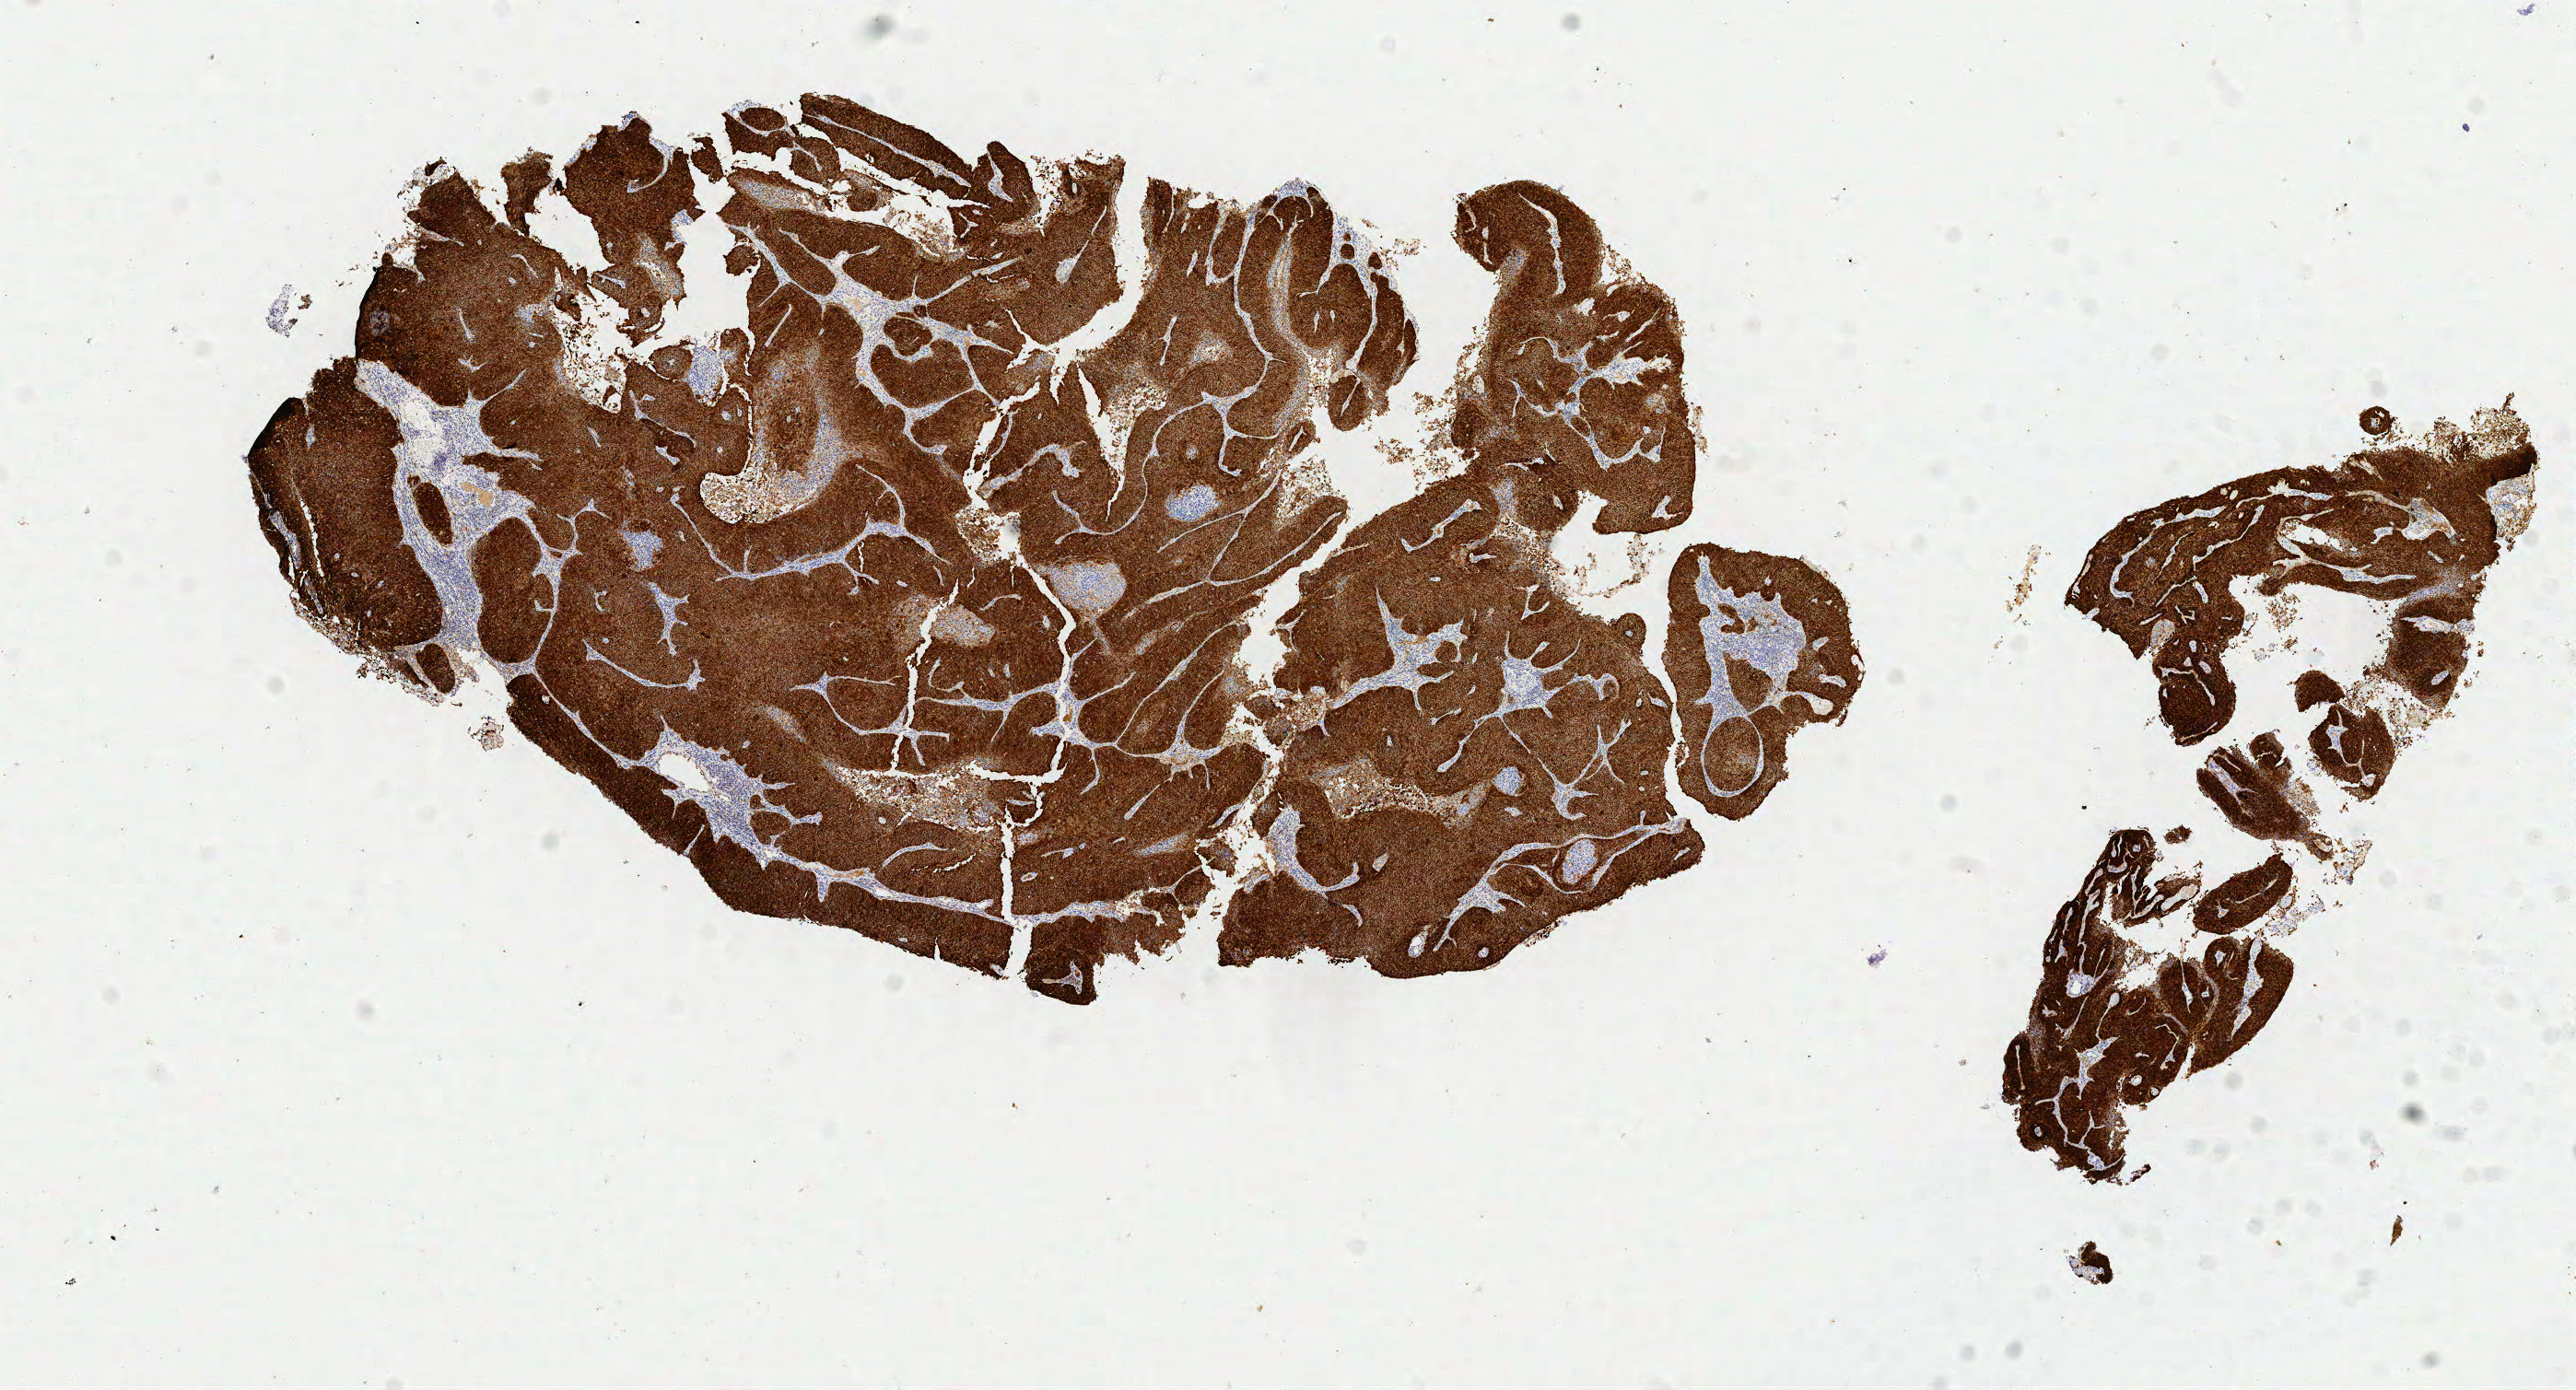
IHC for p16 (p16INK4a), whole-slide image, low-resolution overview of the scanned area, about 11.1 x 6.0 mm, specimen: tumor tissue, anatomic site: cervix. Female patient, aged 56.
Diagnosis: Squamous cell carcinoma, large cell, nonkeratinizing, NOS.